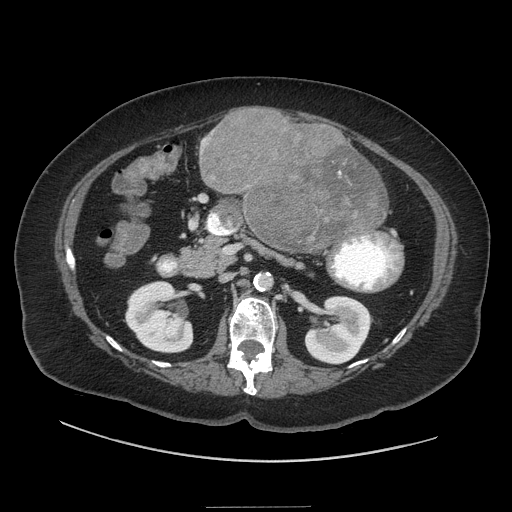
Contrast-enhanced abdominal CT (liver protocol), one axial slice. Reconstruction kernel STANDARD. Soft-tissue window (W 400 / L 40 HU). 512 × 512 image matrix, field of view 440 × 440 mm. From the clinical record (not read from this slice): diagnosis: hepatocellular carcinoma (patient treated with transarterial chemoembolisation; whether this scan precedes or follows treatment is not stated here); TNM stage (as recorded): Stage-II; Child-Pugh class: A.
Structures marked on this image (semi-automatic segmentation, software-assisted and operator-edited):
- liver parenchyma outside the tumour (the mass and vessels are separate outlines, so this box may not span the whole liver): bounding box [x1, y1, x2, y2] px = [199, 108, 386, 238]
- mass: [199, 109, 386, 253]
- liver vessels: [203, 140, 205, 142]